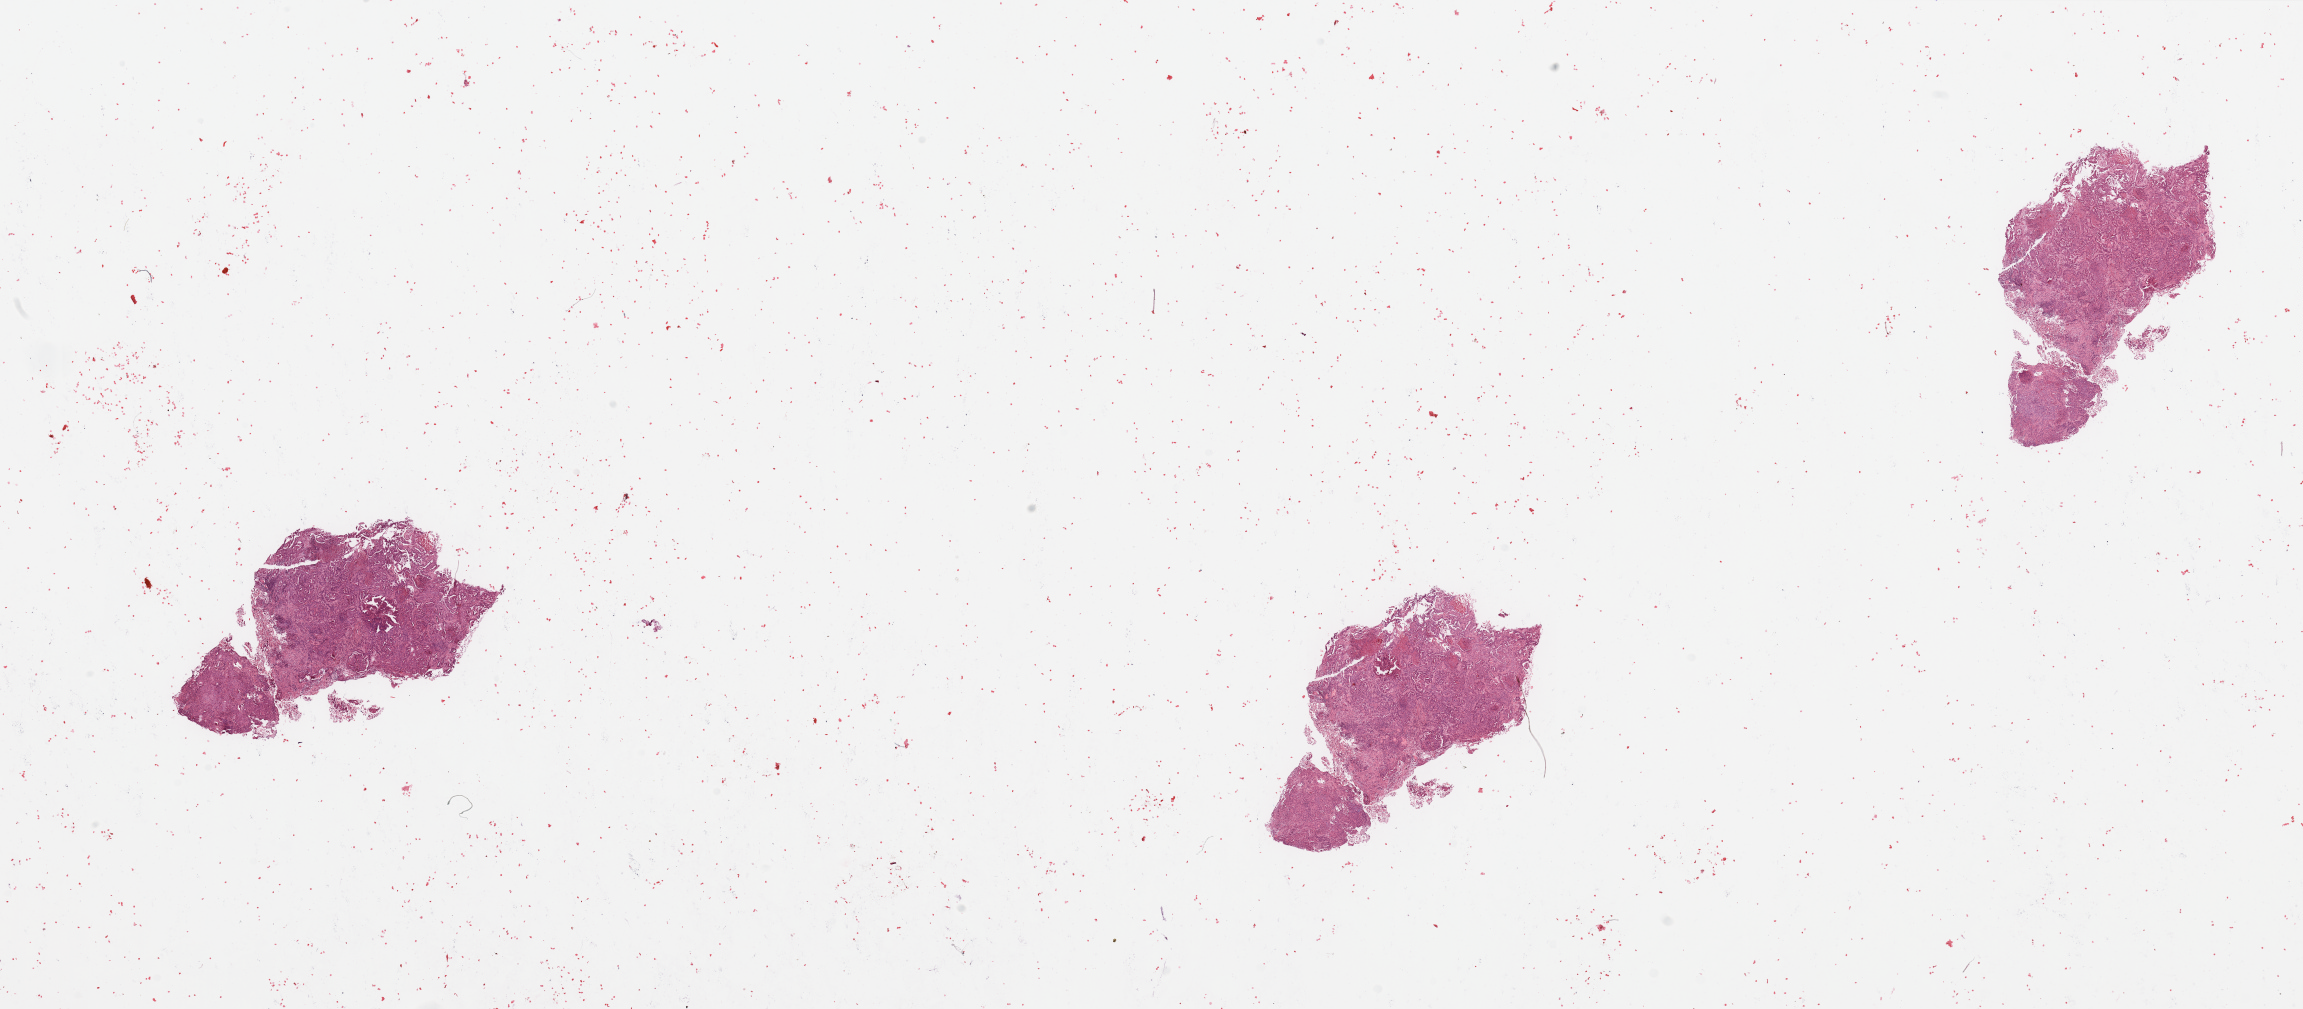
Whole-slide histology image, H&E-stained, a low-resolution overview of the entire scanned area, about 36.4 x 16.0 mm; tumour tissue sample, sampled site: lung. 63-year-old female patient. Histologic grade: G1 (well differentiated). Composition of this section per pathologist review: tumour nuclei 75%, necrosis 3%.
• primary tumour site (as recorded): left upper lobe
• diagnosis: Adenocarcinoma, NOS
• AJCC pathologic stage: IIA